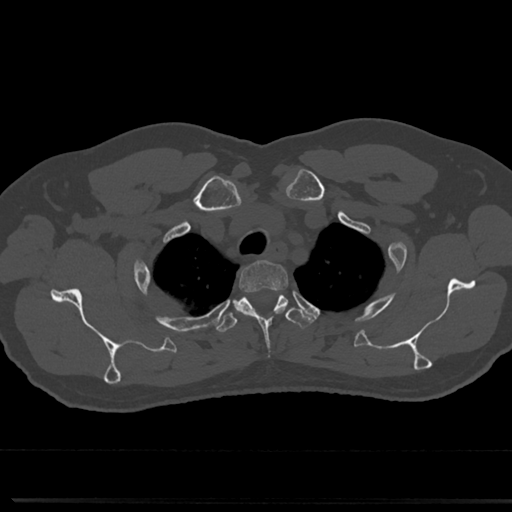
CT including the spine, one axial slice; position 613 of 817 along the scan axis; 120 kVp; bone window (W 1800 / L 400 HU); 0.5 mm slice thickness; 512 × 512 image matrix. Patient: male, 61 years. From the clinical record (not read from this slice): primary cancer: prostate.
Structures marked on this image (semi-automatically segmented with operator editing):
- T2 vertebra: bounding box (x1, y1, x2, y2) in pixels: (239, 261, 289, 289)
- T3 vertebra: (214, 291, 312, 334)